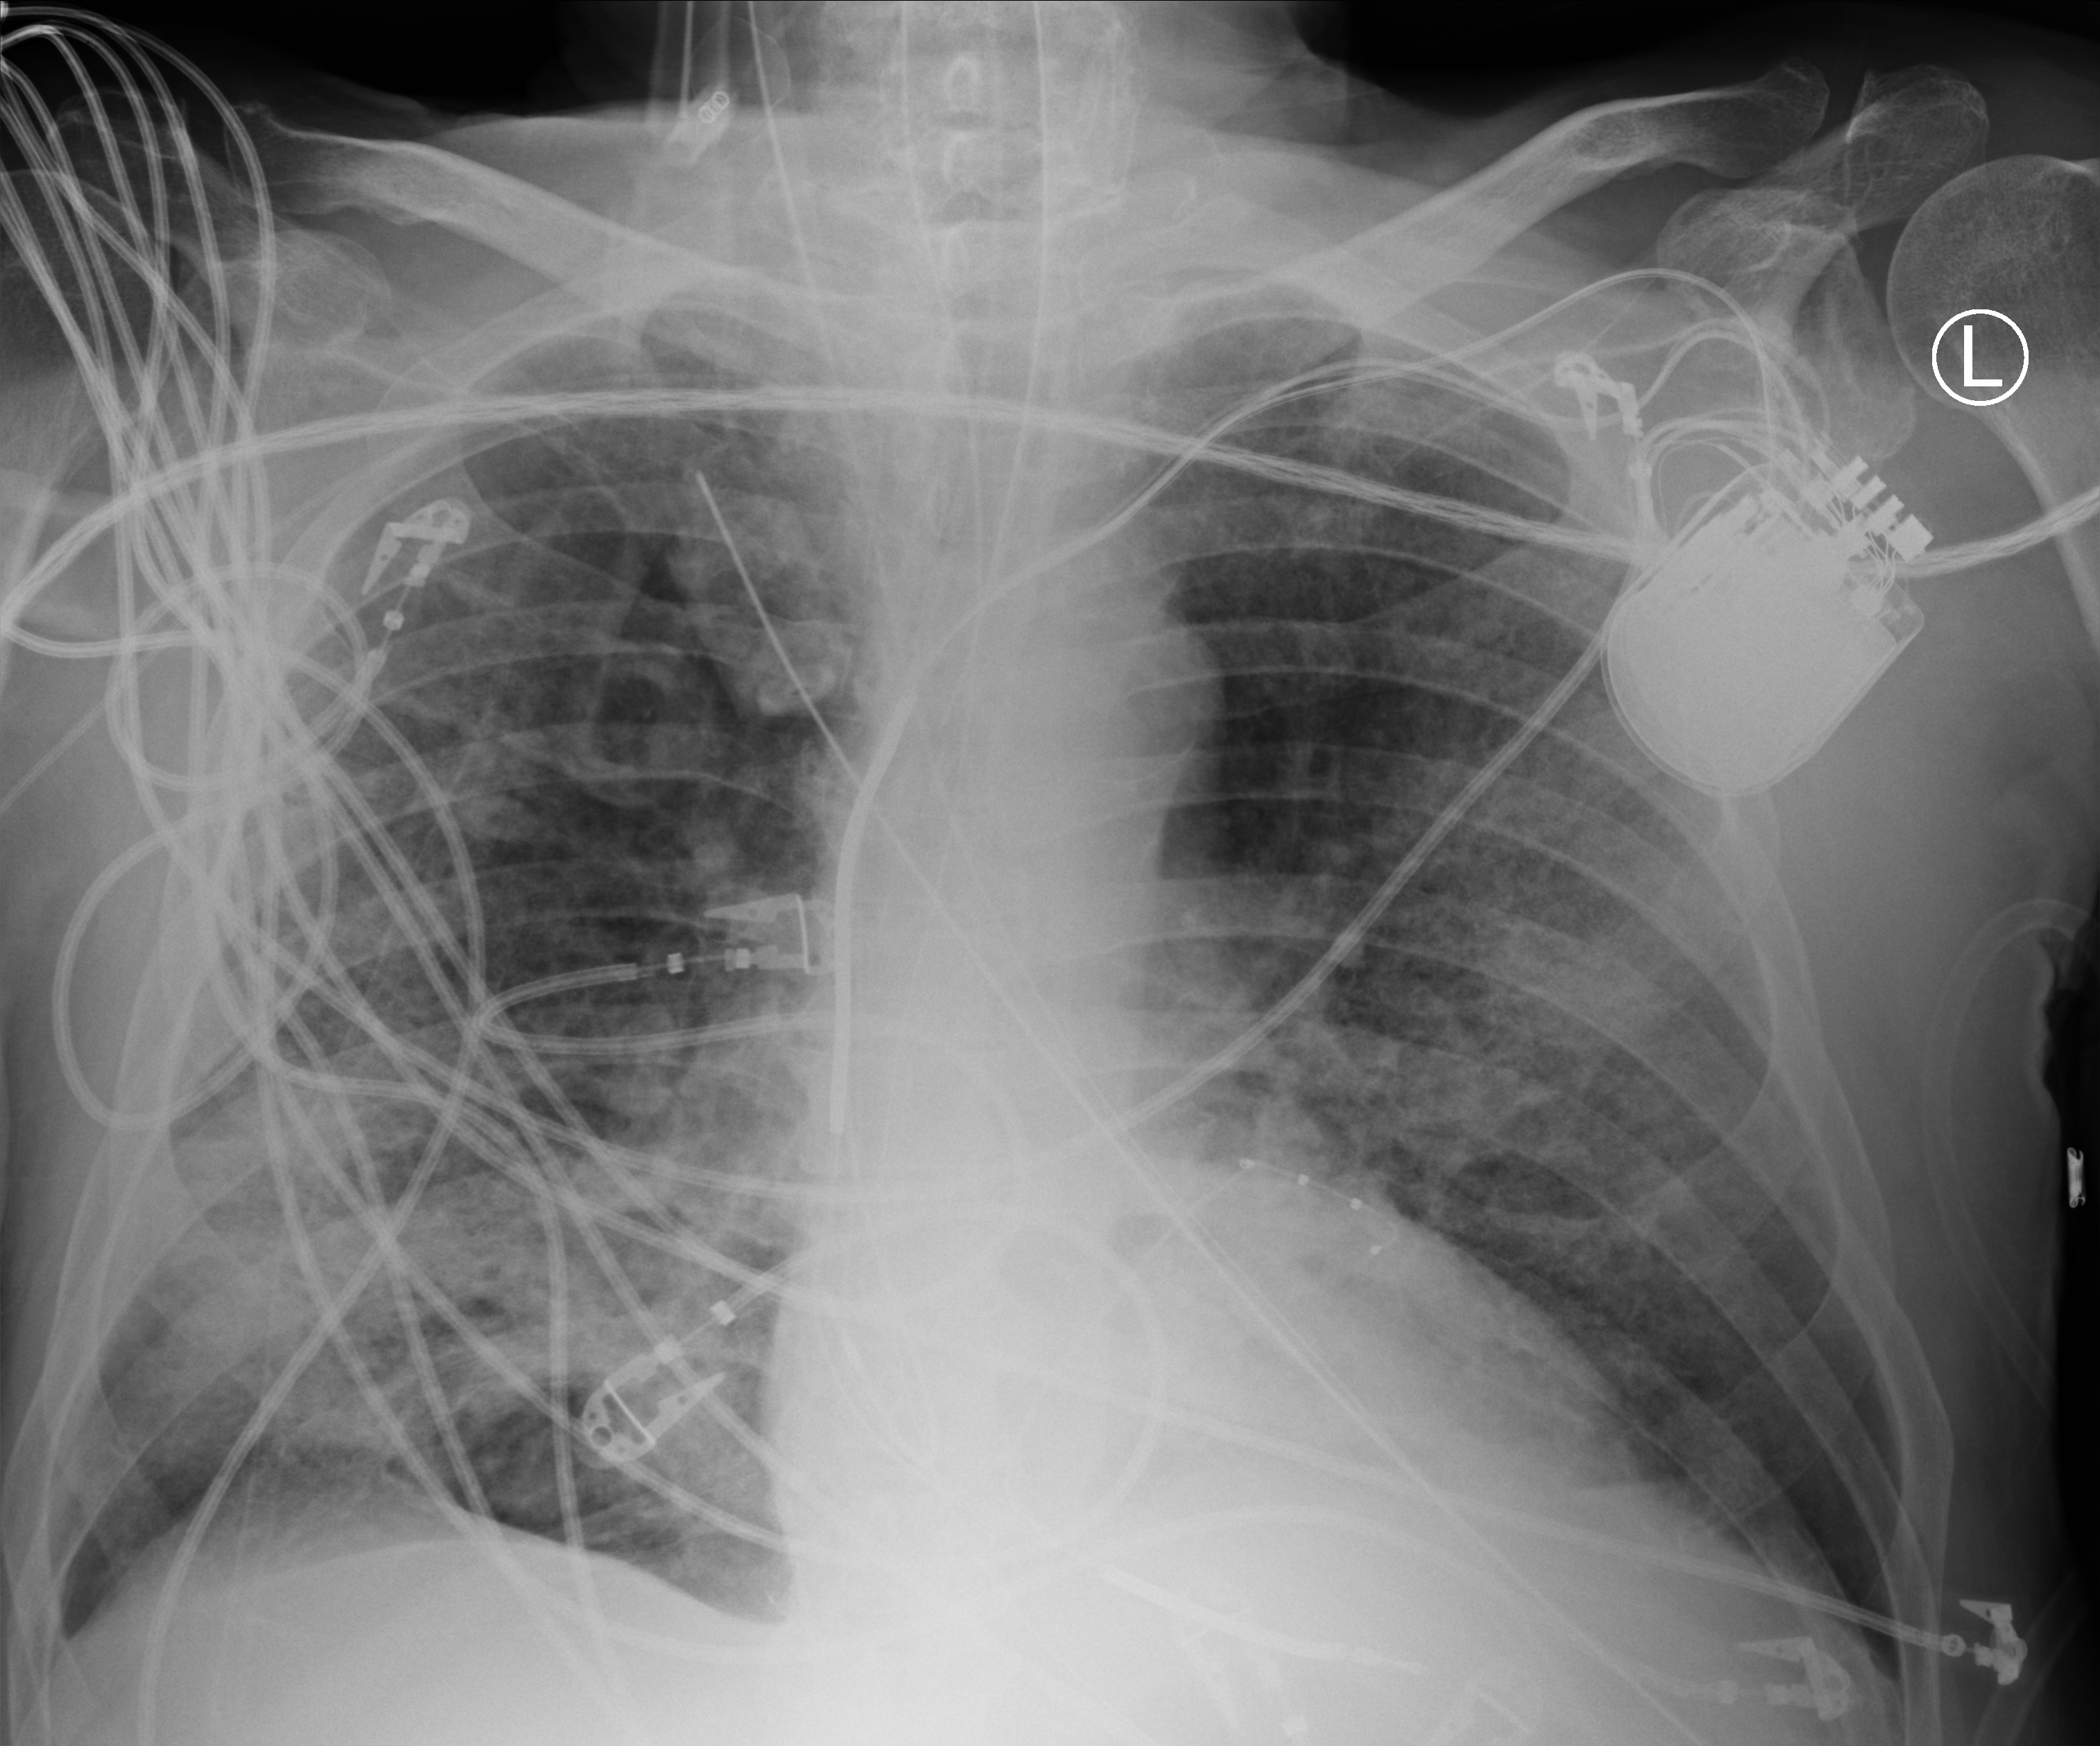
Chest X-ray (portable); anteroposterior (AP) projection. Patient hospitalised with COVID-19; male, aged 60–74 years.
Hospital-stay facts (about this admission, not read from this image; timing relative to this image not recorded): length of hospital stay: 36 days; hypertension (admission record): yes; mechanically ventilated during this hospital stay: yes.